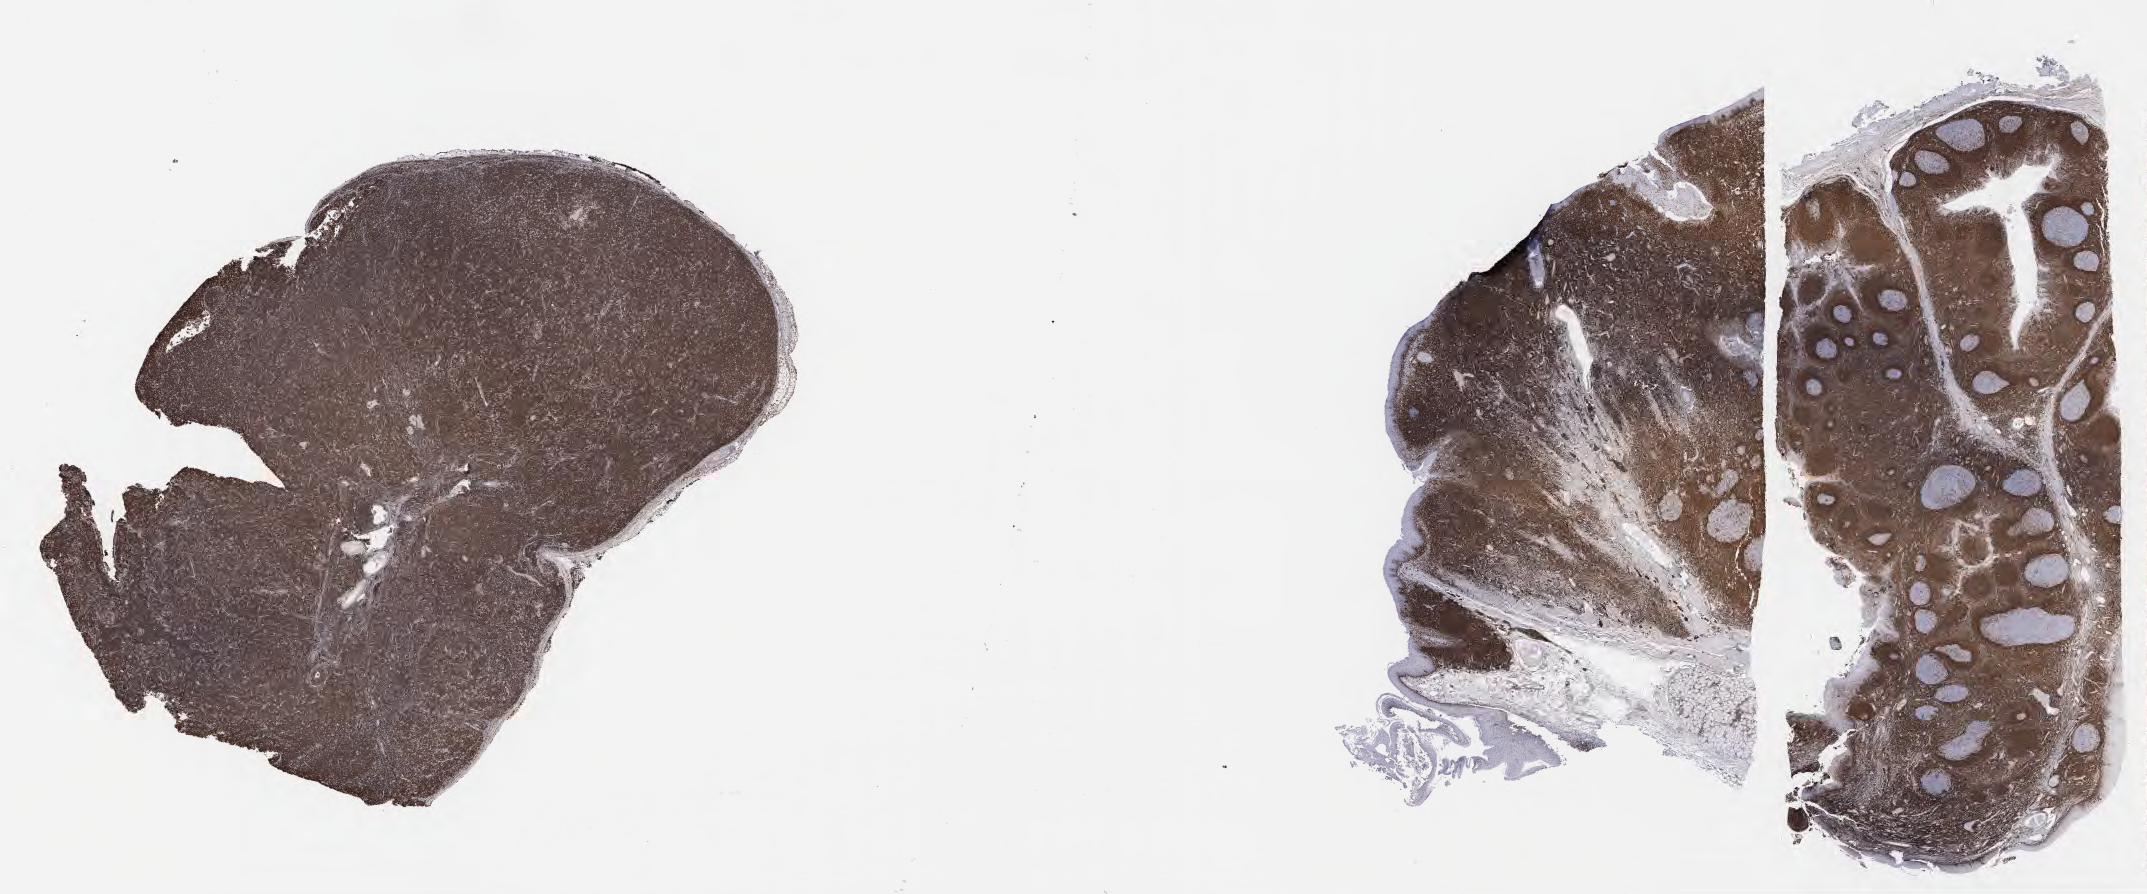
Immunohistochemistry (IHC) whole-slide image stained for BCL2 — whole scanned area (about 34.7 x 14.5 mm) shown as a low-resolution overview; specimen: tumor tissue; site: lymph node. Male patient, aged 32.
• histologic diagnosis: Diffuse large B-cell lymphoma, NOS